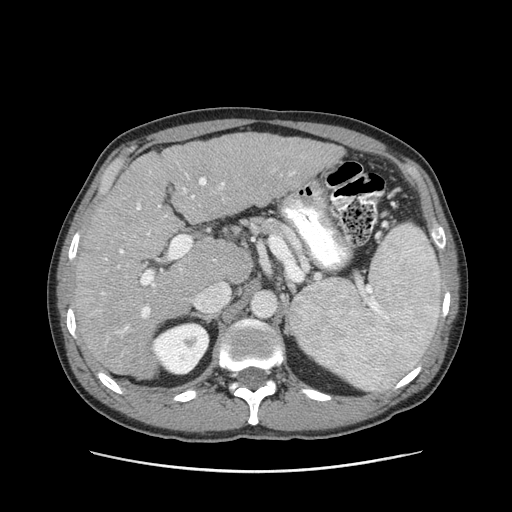
Contrast-enhanced abdominal CT (liver protocol), one axial slice; slice 58 of 93 in the series (ordered by position); 120 kVp; soft-tissue window (W 400 / L 40 HU); 2.5 mm slice thickness; 512 × 512 image matrix, field of view 380 × 380 mm. From the clinical record (not read from this slice): diagnosis: hepatocellular carcinoma (patient treated with transarterial chemoembolisation; whether this scan precedes or follows treatment is not stated here); TNM stage (as recorded): Stage-II.
Annotated regions visible in this slice (semi-automatically segmented with operator editing):
- liver parenchyma outside the tumour (the mass and vessels are separate outlines, so this box may not span the whole liver): bounding box [x1, y1, x2, y2] px = [74, 132, 342, 378]
- liver vessels: [101, 172, 294, 333]